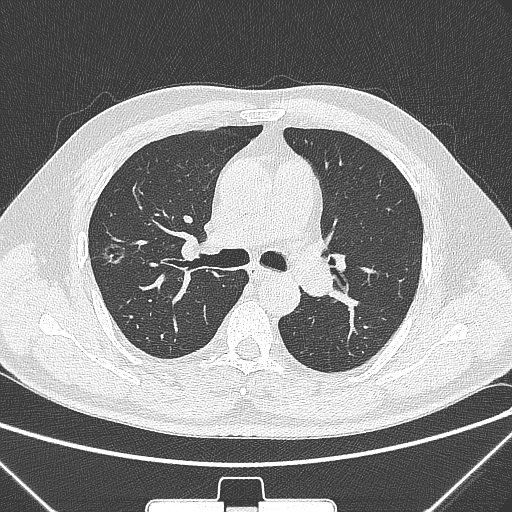
Chest CT, one axial slice; position 194 of 320 along the scan axis; lung window (W 1500 / L -600 HU); 1 mm slice thickness; 512 × 512 image matrix, field of view 350 × 350 mm. Male patient, age 58 years. Case-level facts recorded for this patient, not image findings: clinical TNM (as recorded): T1c N0 M0; histopathological grade: G2.
Annotated regions visible in this slice (rectangle marked by the reading radiologist):
- lung tumour (recorded histology: adenocarcinoma): bounding box <99,233,133,278> (left, top, right, bottom; pixels)